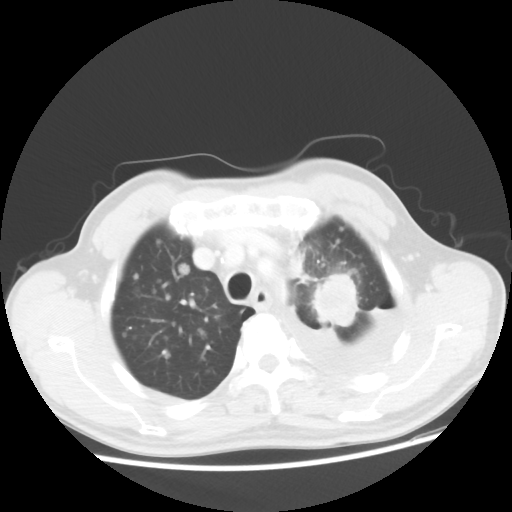
Chest CT, one axial slice; position 39 of 48 along the scan axis; reconstruction kernel STANDARD; lung window (W 1500 / L -600 HU); 5 mm slice thickness; 512 × 512 image matrix, field of view 362 × 362 mm. Male patient, age 55 years. From the clinical record (not read from this slice): clinical TNM (as recorded): T2 N3 M1a; histopathological grade: G3.
Structures marked on this image (rectangle marked by the reading radiologist):
- lung tumour (recorded histology: squamous cell carcinoma): bounding box <310,270,363,336> (left, top, right, bottom; pixels)